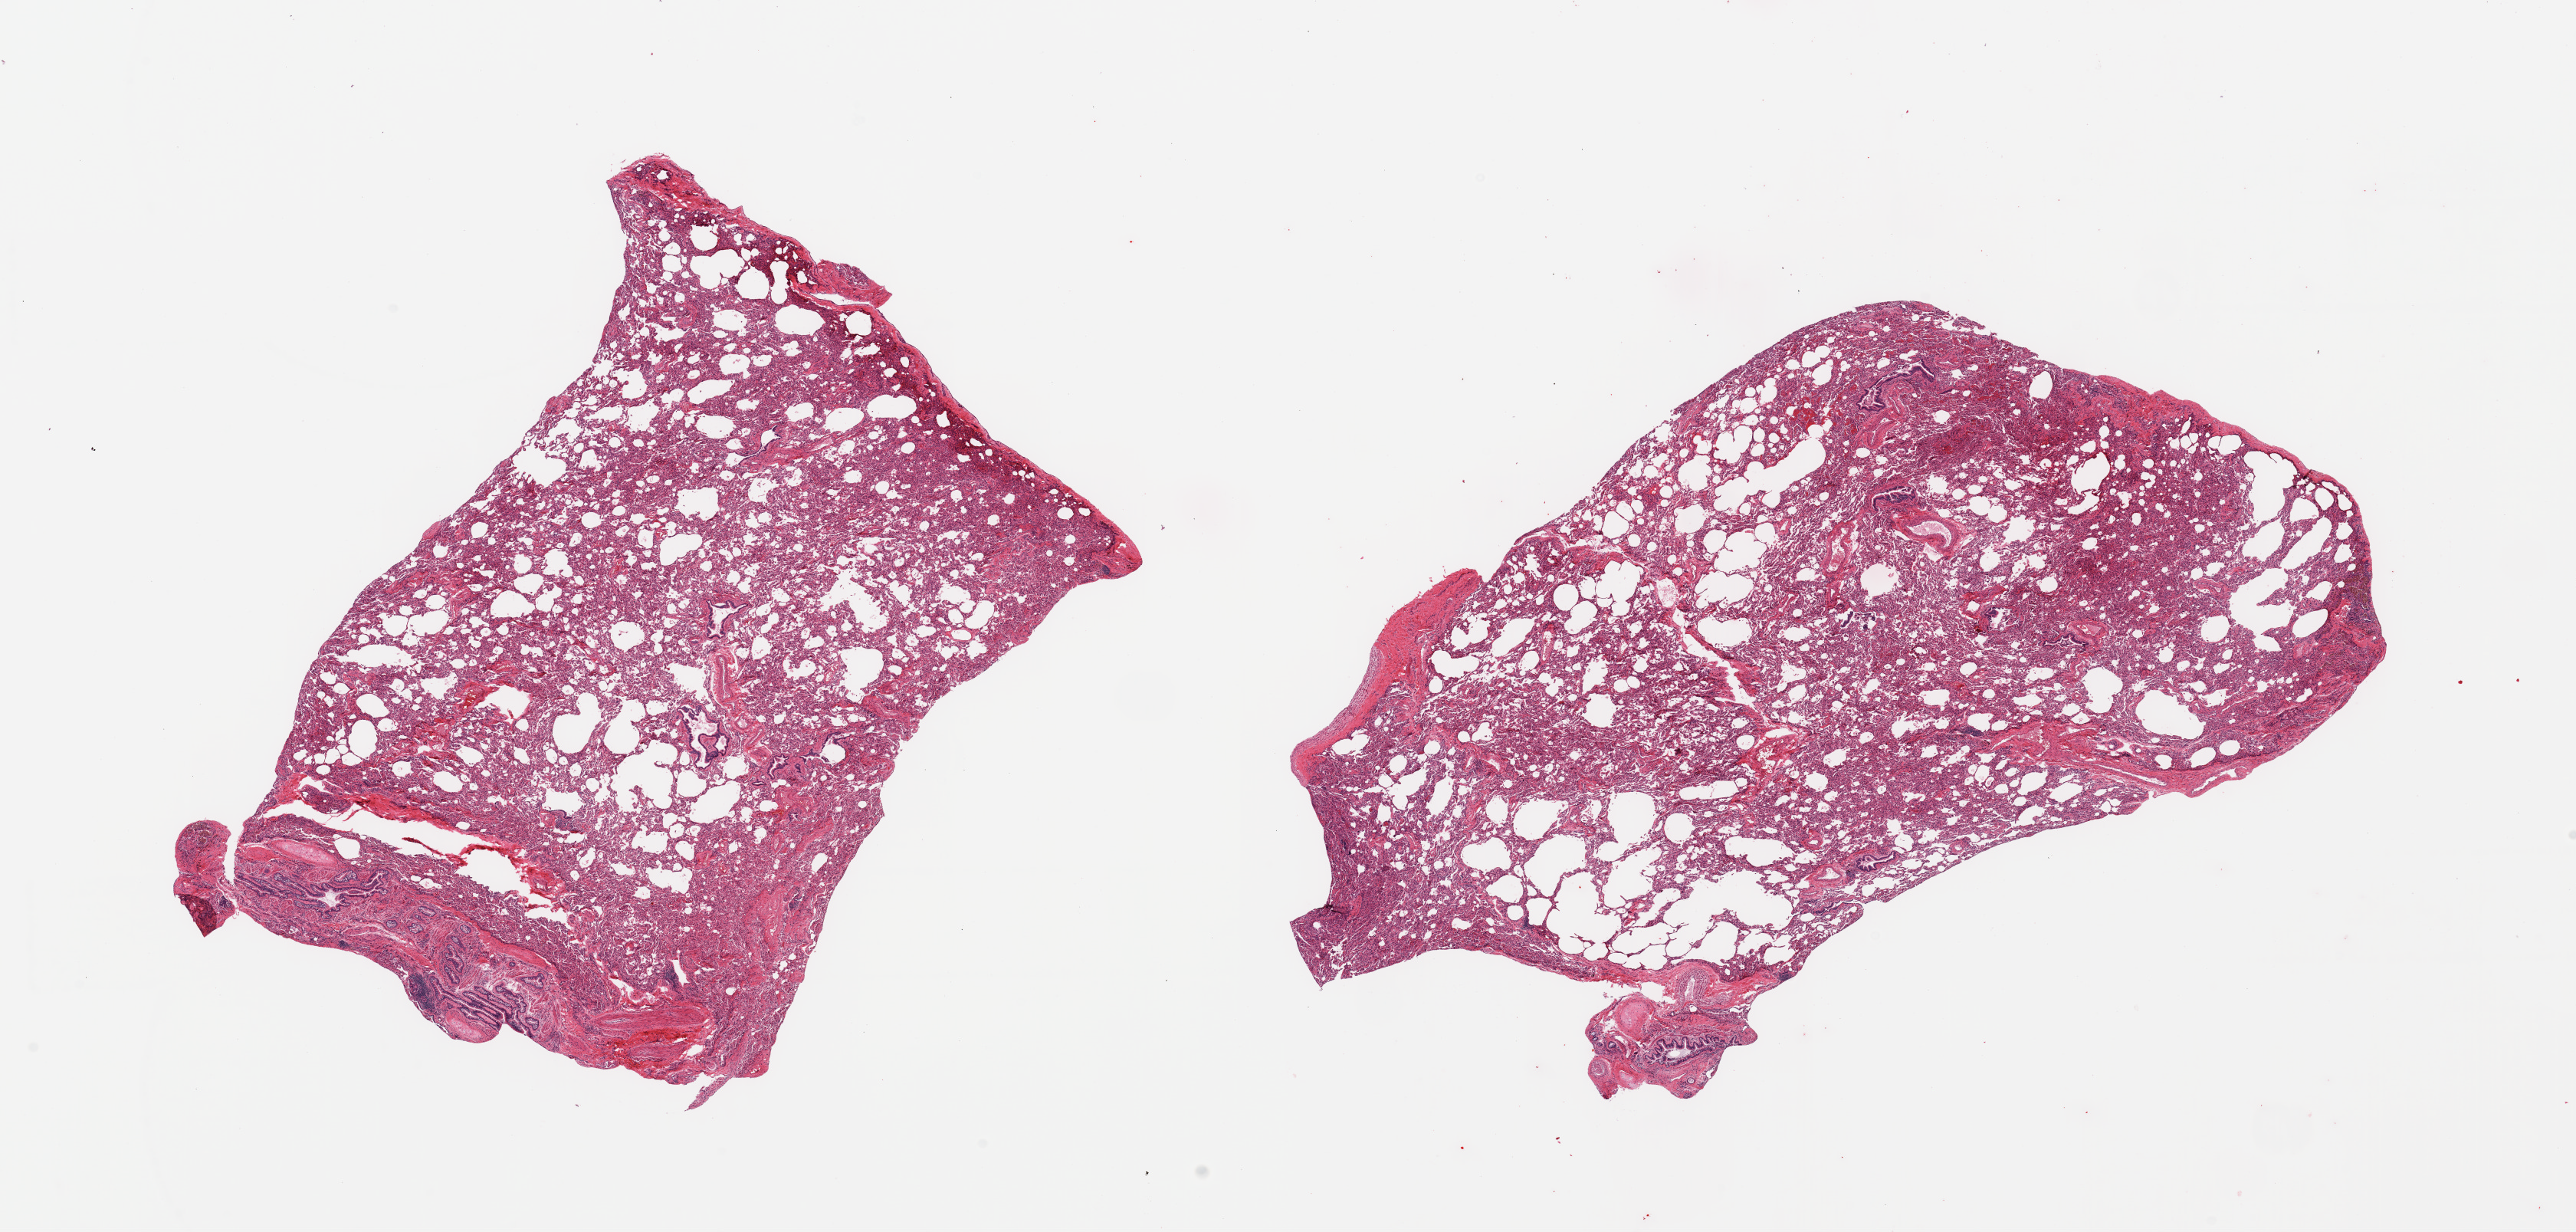
Digitized haematoxylin and eosin-stained section — whole scanned area (about 26.6 x 12.7 mm, slide scanned at 20x) shown as a low-resolution overview. PAXgene-fixed paraffin-embedded (PFPE) section. Sampled site (target tissue): lung. Donor tissue sample. Male donor.
Pathologist's review note for this sample: 2 pieces; includes pleura, atelectasis with patchy widened airspaces, bronchopneumonia, pulmonary macrophages, portion of bronchus/cartilage.